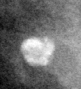
Crop from a digitized film mammogram around one marked abnormality; left breast; MLO view.
- Finding: calcifications, morphology lucent center; BI-RADS assessment category 2; subtlety rating 4 on a 1 (subtle) to 5 (obvious) scale; benign; no additional work-up was recommended (benign without callback).